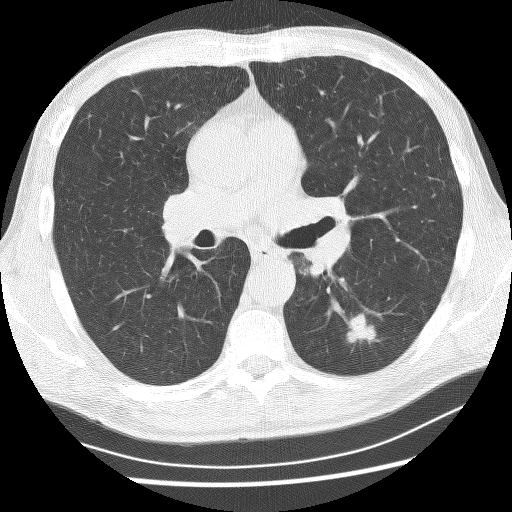
Low-dose screening chest CT, one axial slice. Slice 142 of 253 in the series (ordered by position). Reconstruction kernel BONE. 120 kVp. Lung window (W 1500 / L -600 HU). 2.5 mm slice thickness. 512 × 512 image matrix, field of view 340 × 340 mm.
Outlined on this slice (outlined manually by an expert reader):
- lesion 1 (tumor, lower lobe of left lung): bounding box [x1, y1, x2, y2] px = [347, 314, 376, 343]